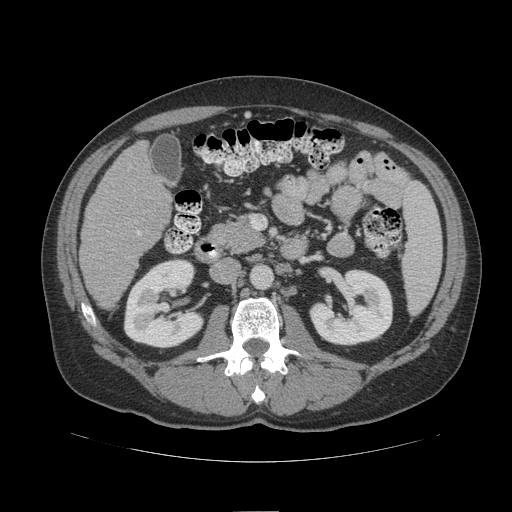
Contrast-enhanced abdominal CT (liver protocol), one axial slice. Position 44 of 109 along the scan axis. Soft-tissue window (W 400 / L 40 HU). 512 × 512 image matrix, field of view 420 × 420 mm. Case-level facts recorded for this patient, not image findings: diagnosis: hepatocellular carcinoma (patient treated with transarterial chemoembolisation; whether this scan precedes or follows treatment is not stated here); TNM stage (as recorded): Stage-IIIB; Child-Pugh class: A; tumour differentiation: poorly differentiated.
Annotated regions visible in this slice (semi-automatically segmented with operator editing):
- liver parenchyma outside the tumour (the mass and vessels are separate outlines, so this box may not span the whole liver): box from (x=80, y=140) to (x=172, y=308) px
- liver vessels: (x=137, y=231)–(x=140, y=234)